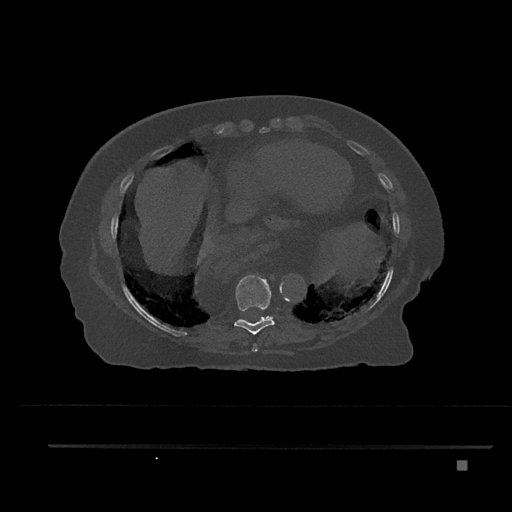
CT including the spine, one axial slice; slice 395 of 797 in the series (ordered by position); bone window (W 1800 / L 400 HU); 0.5 mm slice thickness; 512 × 512 image matrix. Patient: female, 76 years. Case-level facts recorded for this patient, not image findings: primary cancer: lung.
Structures marked on this image (semi-automatically segmented with operator editing):
- T8 vertebra: box from (x=252, y=343) to (x=258, y=352) px
- T9 vertebra: (x=234, y=275)–(x=276, y=335)